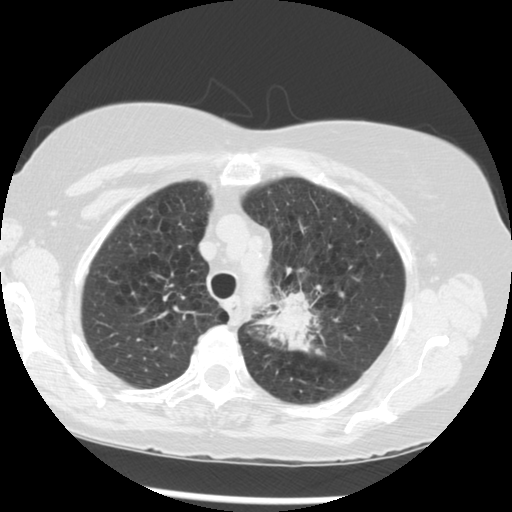
Low-dose screening chest CT, axial slice; third annual screen; lung window (W 1500 / L -600 HU); 120 kVp. Female participant, aged 70 years at enrolment.
Expert-annotated lung lesion, box from (x=260, y=274) to (x=355, y=363) px. Reader record for this screening exam (exam-level; its link to the box is not recorded): non-calcified nodule or mass ≥4 mm, left upper lobe, 32 × 26 mm, spiculated (stellate) margins, soft tissue attenuation, pre-existing on the prior screen: yes; interval growth: yes. Official screen result: positive, other. Lung cancer was diagnosed 24 days after this screen: neoplasm, malignant, left upper lobe, stage IIIB (AJCC 6th edition), 40 mm at pathology.